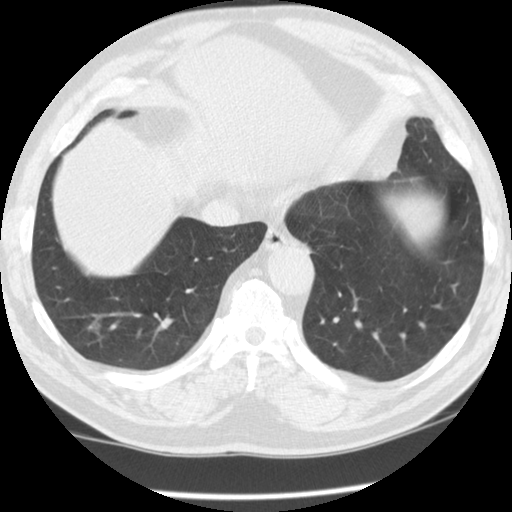
Chest CT (low-dose screening protocol), one axial image, second screening round (one year after baseline), lung window (W 1500 / L -600 HU), 2.5 mm slice thickness, 120 kVp. Male participant, aged 62 years at enrolment.
- Expert reader's lesion annotation, box from (x=64, y=303) to (x=121, y=359) px.
- Screening reader's record for this exam (one nodule recorded; not confirmed to be the boxed lesion): non-calcified nodule or mass ≥4 mm, right lower lobe, 13 × 11 mm, smooth margins, ground glass attenuation, pre-existing on the prior screen: yes; interval growth: no.
- Later outcome: lung cancer diagnosed 330 days after this screen — bronchiolo-alveolar carcinoma, non-mucinous, right lower lobe, well differentiated (G1), stage IA (AJCC 6th edition), 14 mm at pathology.